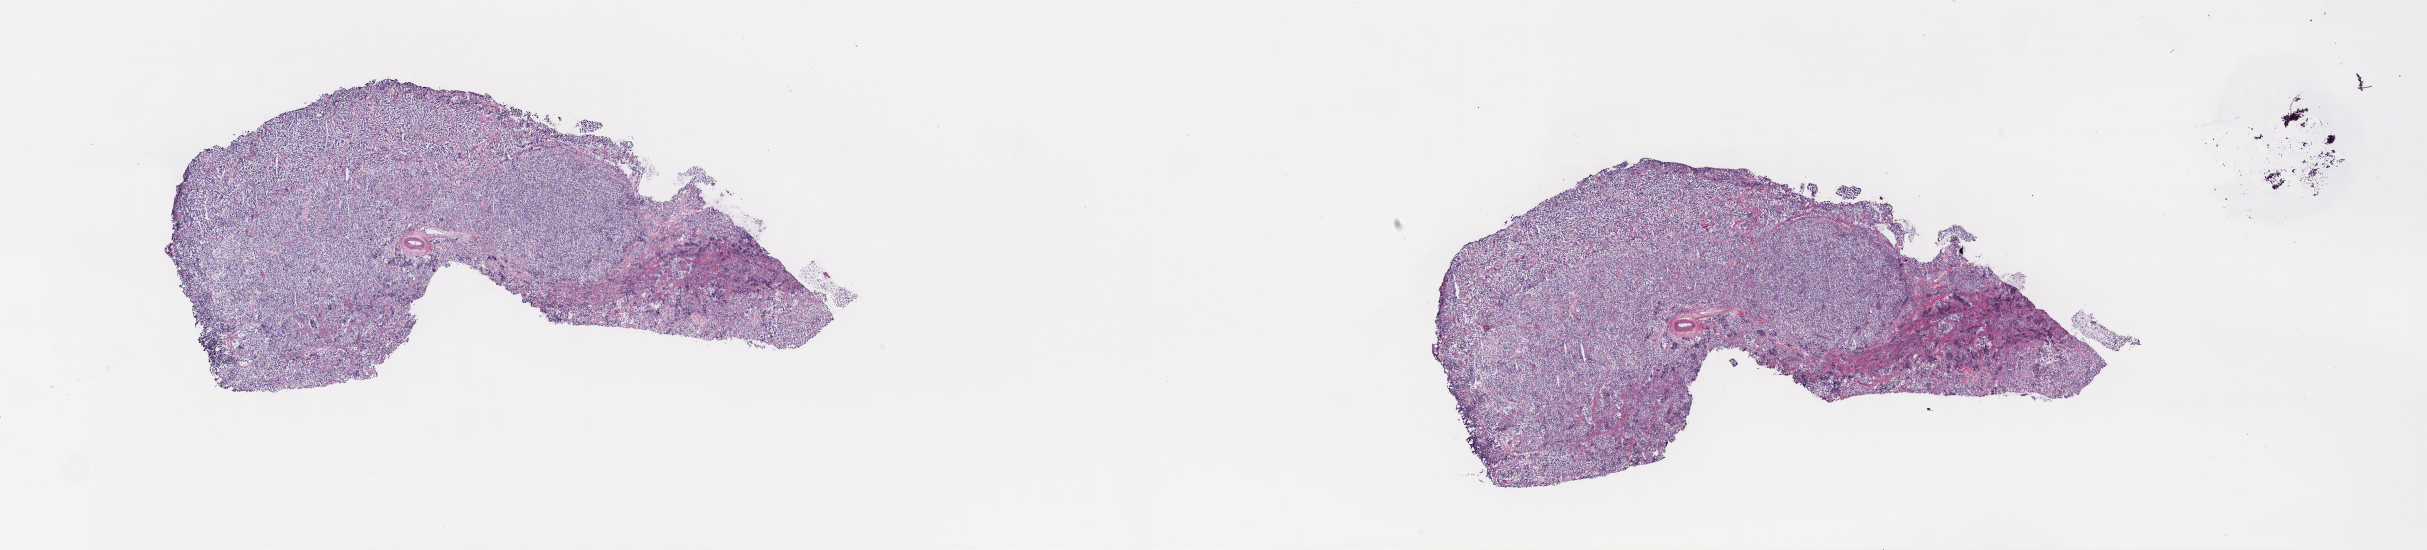
Whole-slide histology image, H&E — low-resolution overview of the scanned area, about 39.3 x 8.9 mm (slide scanned at 40x), frozen section, testis, primary tumour sample. Patient: male, age at initial diagnosis 27 years. Pathologist review of this section (percent, as recorded): tumour cells 80%, tumour nuclei 80%, normal cells 0%, stromal cells 20%, necrosis 0%. Infiltration values recorded for this section: lymphocyte infiltration 70%, monocyte infiltration 25%, neutrophil infiltration 0%.
* TNM: T1 NX M0
* histologic diagnosis: Seminoma, NOS
* laterality: left
* AJCC pathologic stage: IS (7th edition)